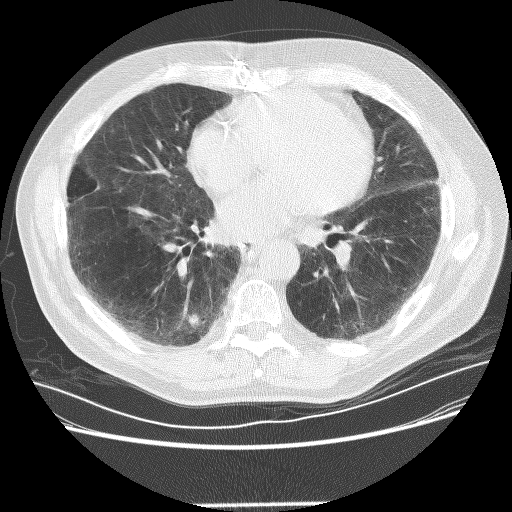
Axial slice from a low-dose chest CT screening exam, baseline annual screen, lung window (W 1500 / L -600 HU), 2.5 mm slice thickness, lung (sharp) reconstruction kernel (BONE), 120 kVp. Male participant, aged 72 years at enrolment. Former smoker at enrolment.
• Lesion marked by an expert reader, bounding box <171,307,210,343> (left, top, right, bottom; pixels).
• The screening reader recorded 2 non-calcified nodules or masses ≥4 mm on this exam (right lower lobe, left lower lobe); which of them this box marks is not recorded.
• Later outcome: lung cancer diagnosed 436 days after this screen (after the second annual screen) — squamous cell carcinoma, NOS, right lower lobe, poorly differentiated (G3), stage IB (AJCC 6th edition), 42 mm at pathology.